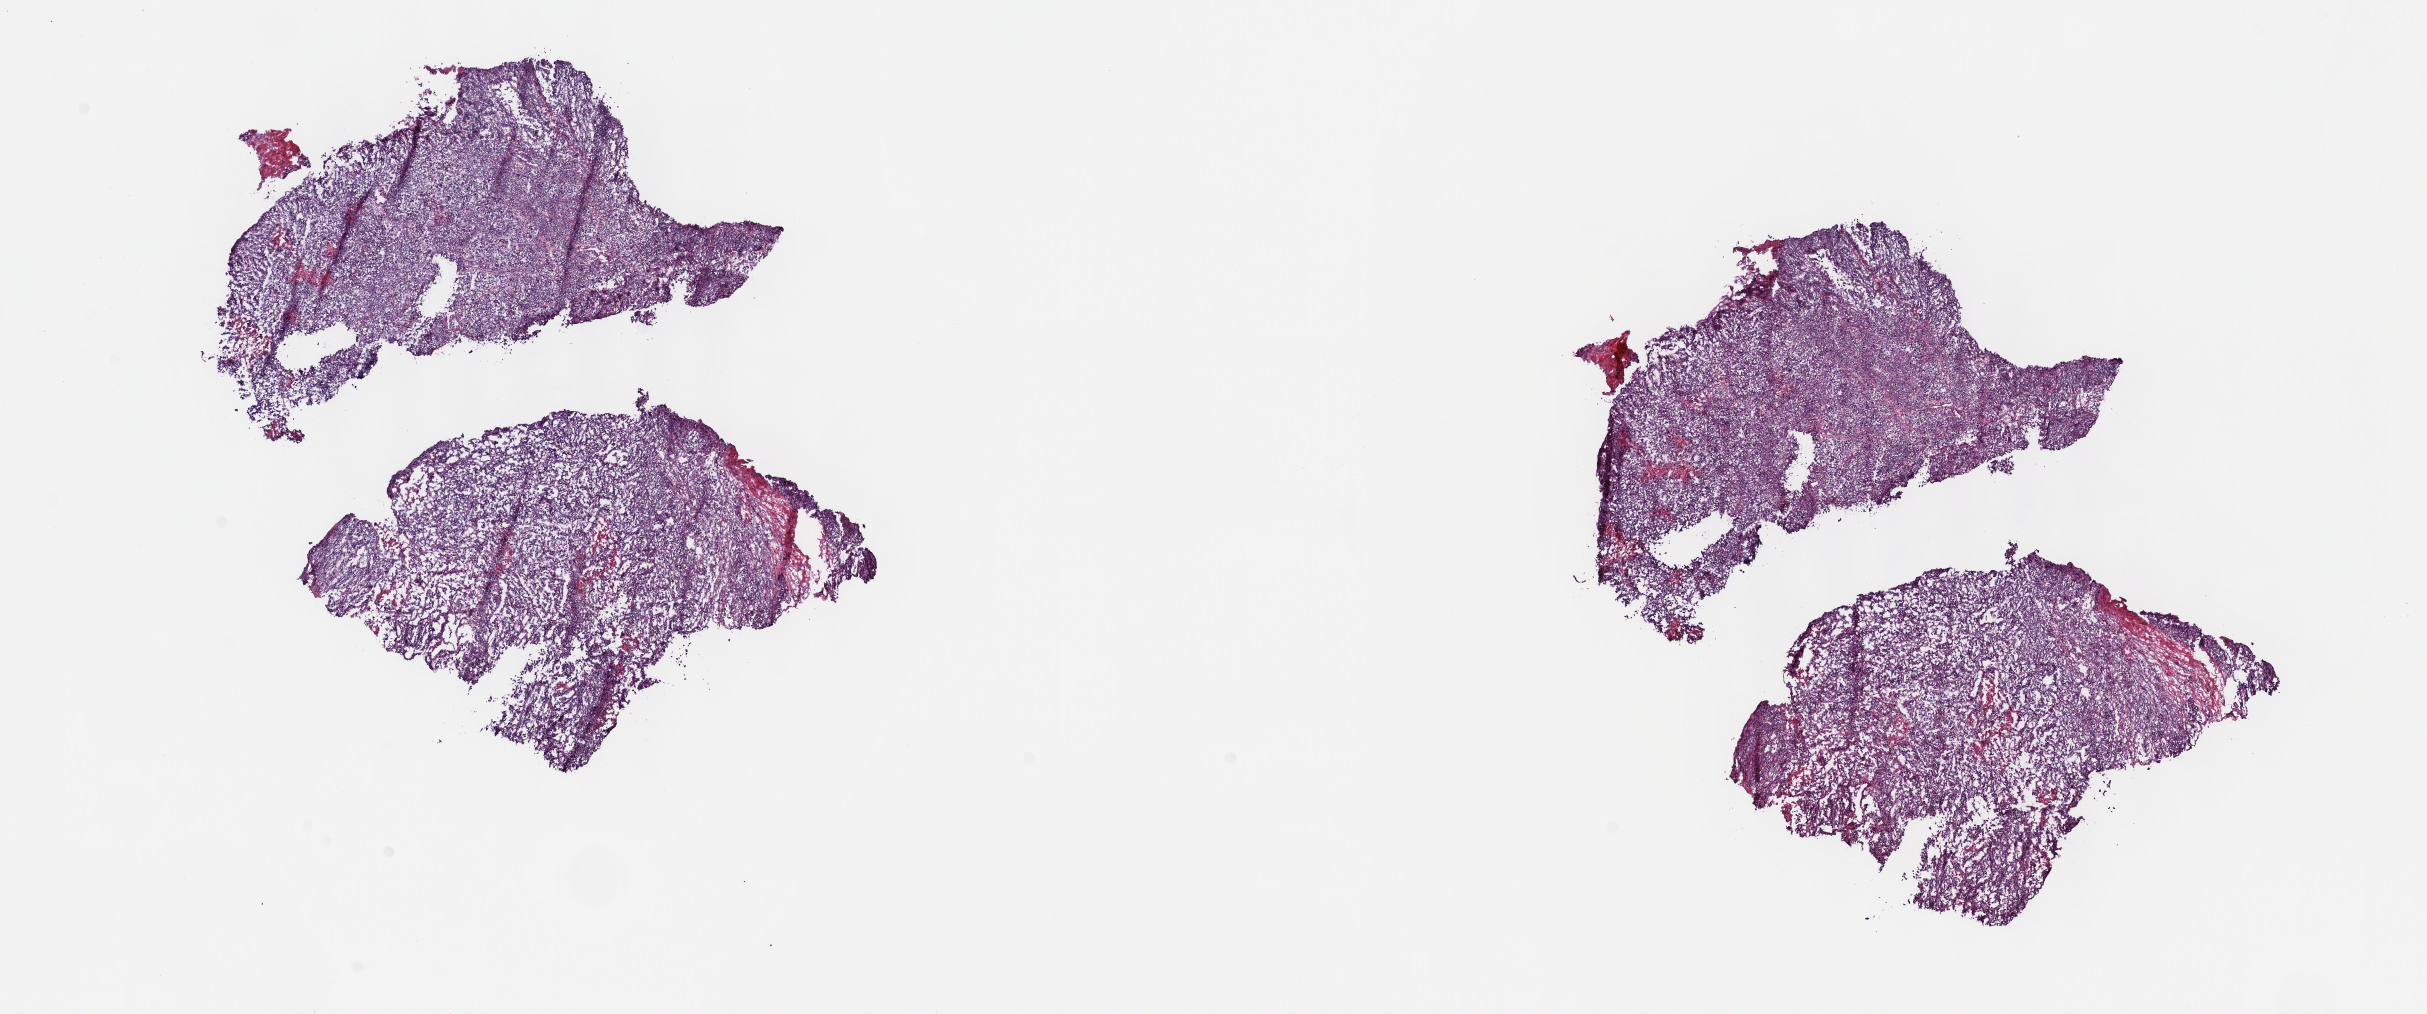
Digitized Hematoxylin and eosin (H&E) stained tissue section (whole slide) — a low-resolution overview of the entire scanned area, about 19.6 x 8.2 mm (acquisition: 40x scan), frozen section from the top of the tissue portion, metastatic tumour sample, sampled site: lymph nodes of axilla or arm. Patient: male, age at initial diagnosis 45 years. Pathologist review of this section (percent, as recorded): tumour cells 70%, tumour nuclei 90%, normal cells 0%, stromal cells 15%, necrosis 15%. Inflammatory infiltration, as recorded: lymphocyte infiltration 0%, monocyte infiltration 0%, neutrophil infiltration 0%.
This section: metastatic tumour tissue. Patient diagnosis: Malignant melanoma, NOS.